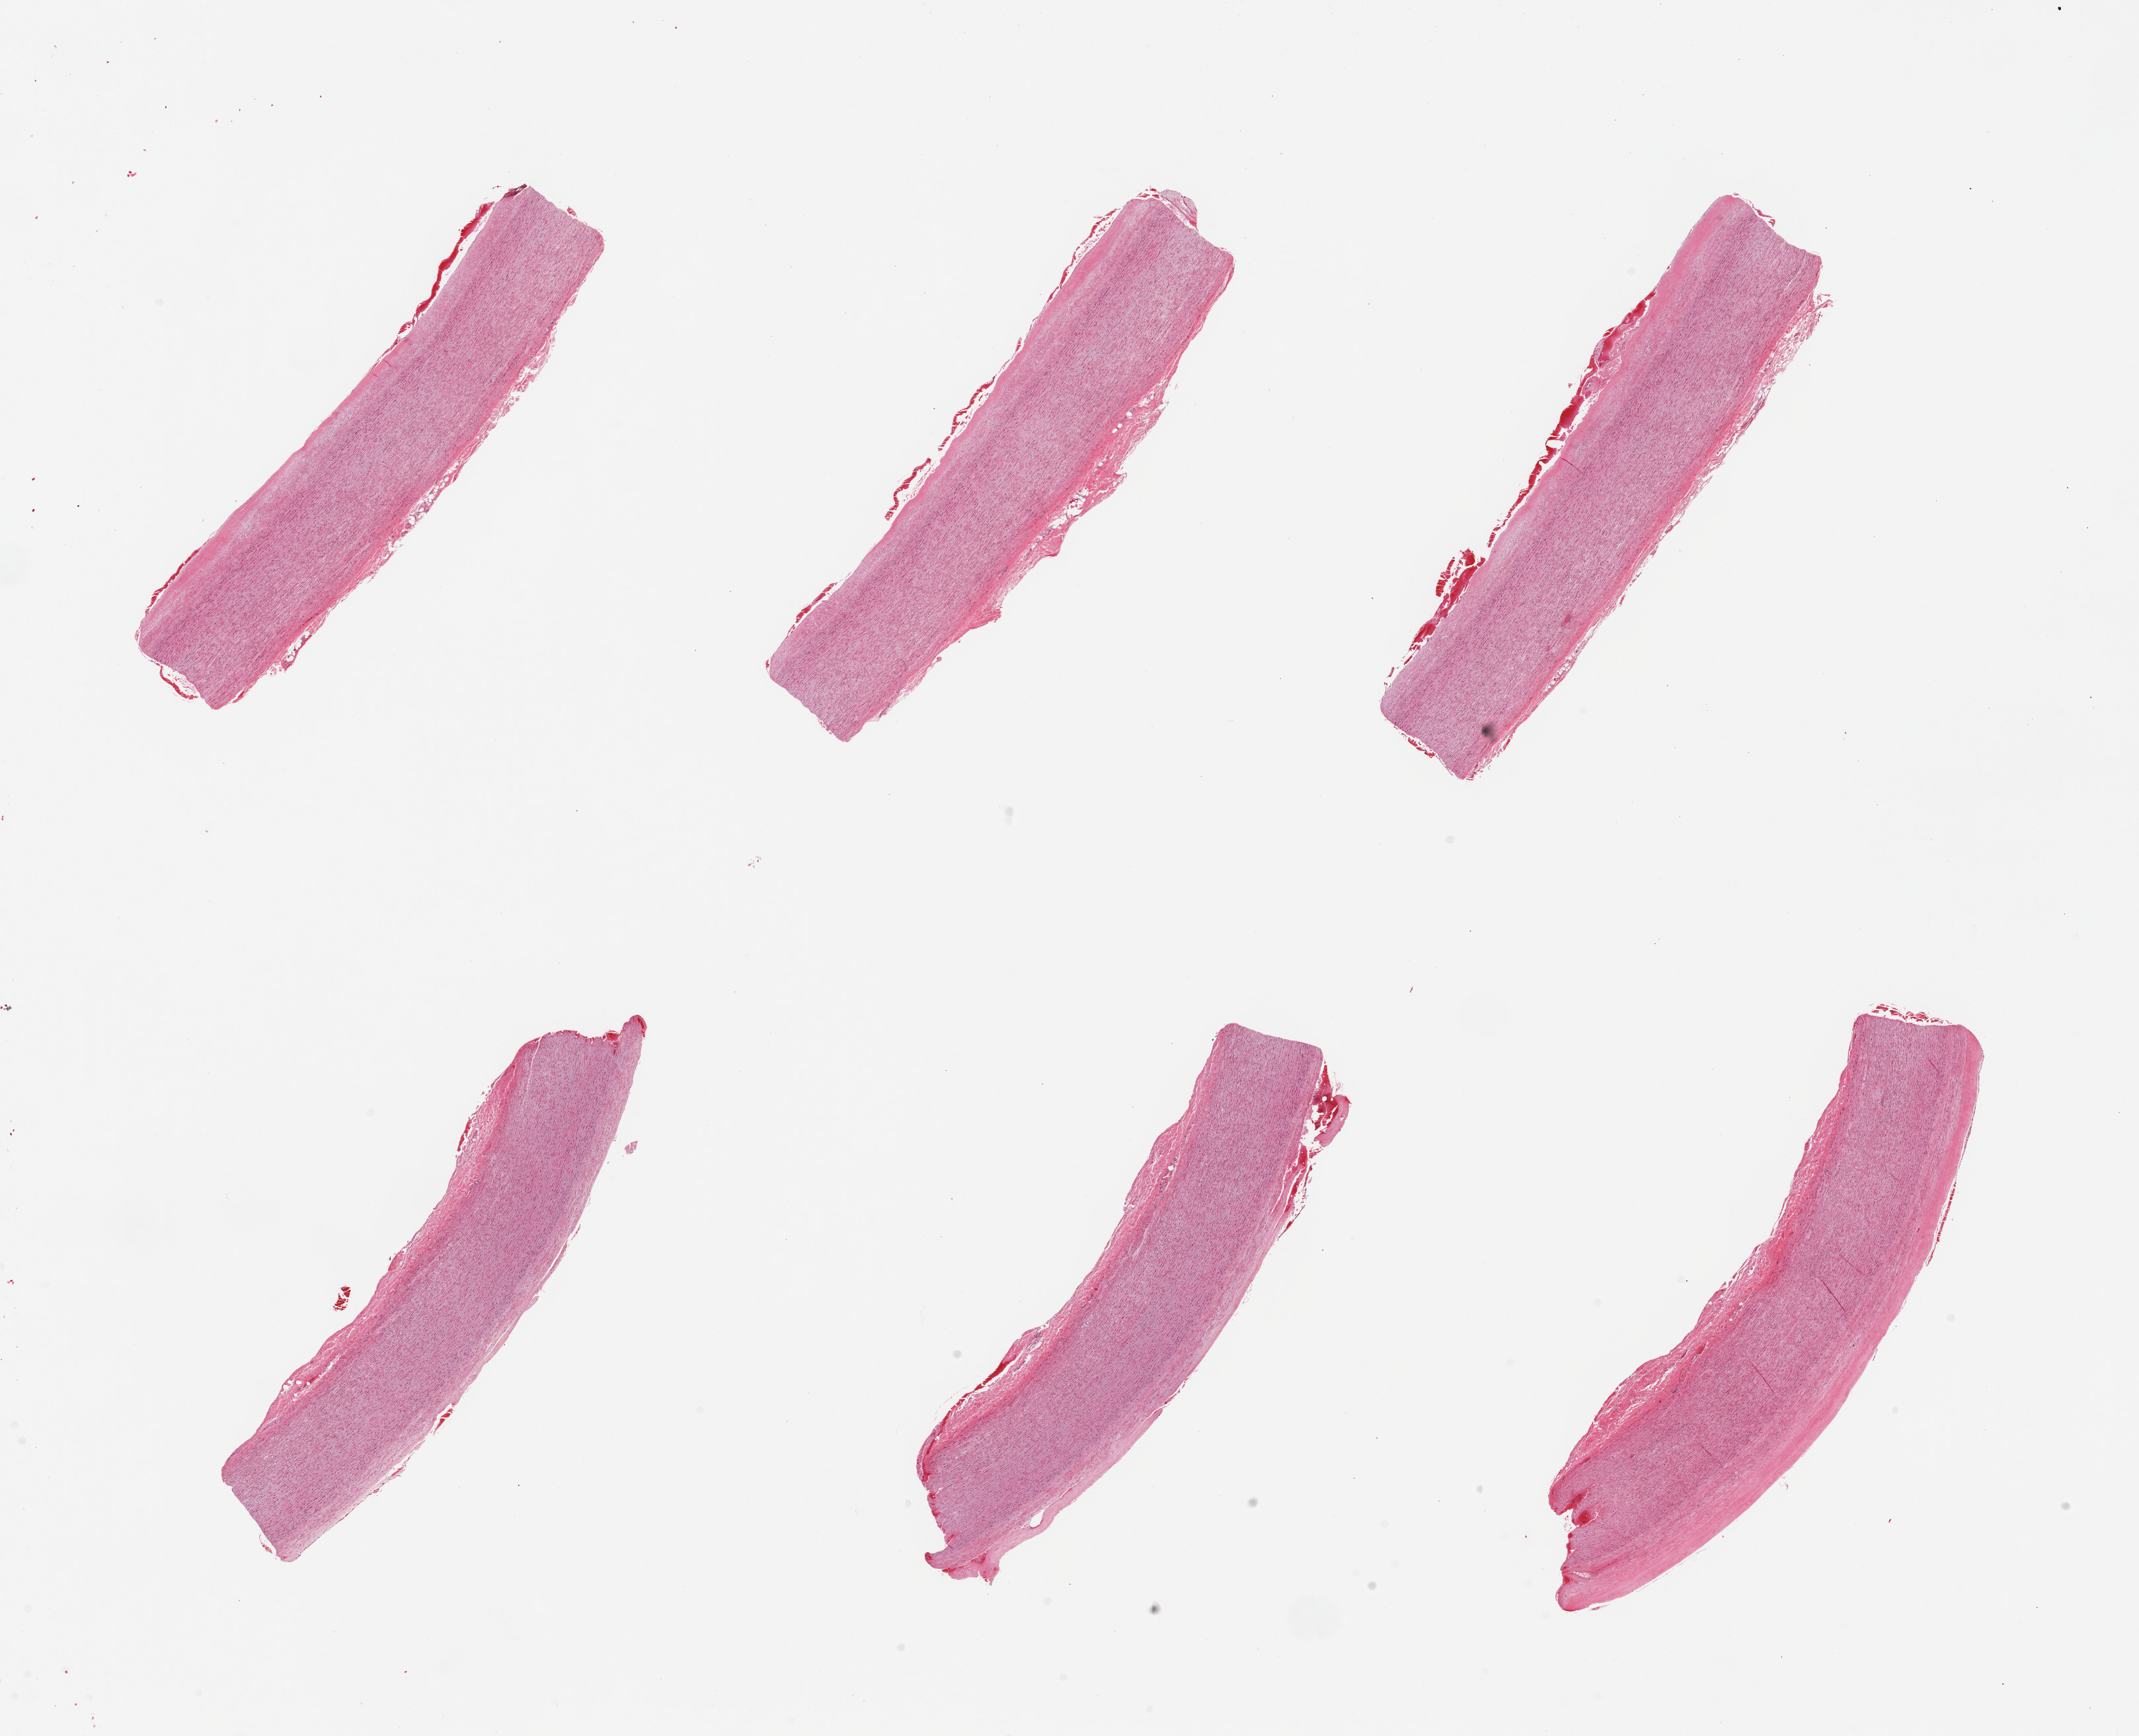
Whole-slide image, H&E stain, shown as a low-resolution overview of the whole scanned area (about 25.6 x 20.8 mm, slide scanned at 20x). PAXgene-fixed paraffin-embedded (PFPE) section. Section of aorta (target tissue). Donor tissue sample. Donor: male.
Pathologist's review note for this sample: 6 pieces; atherosclerotic plaque with focal superficial thrombosis.